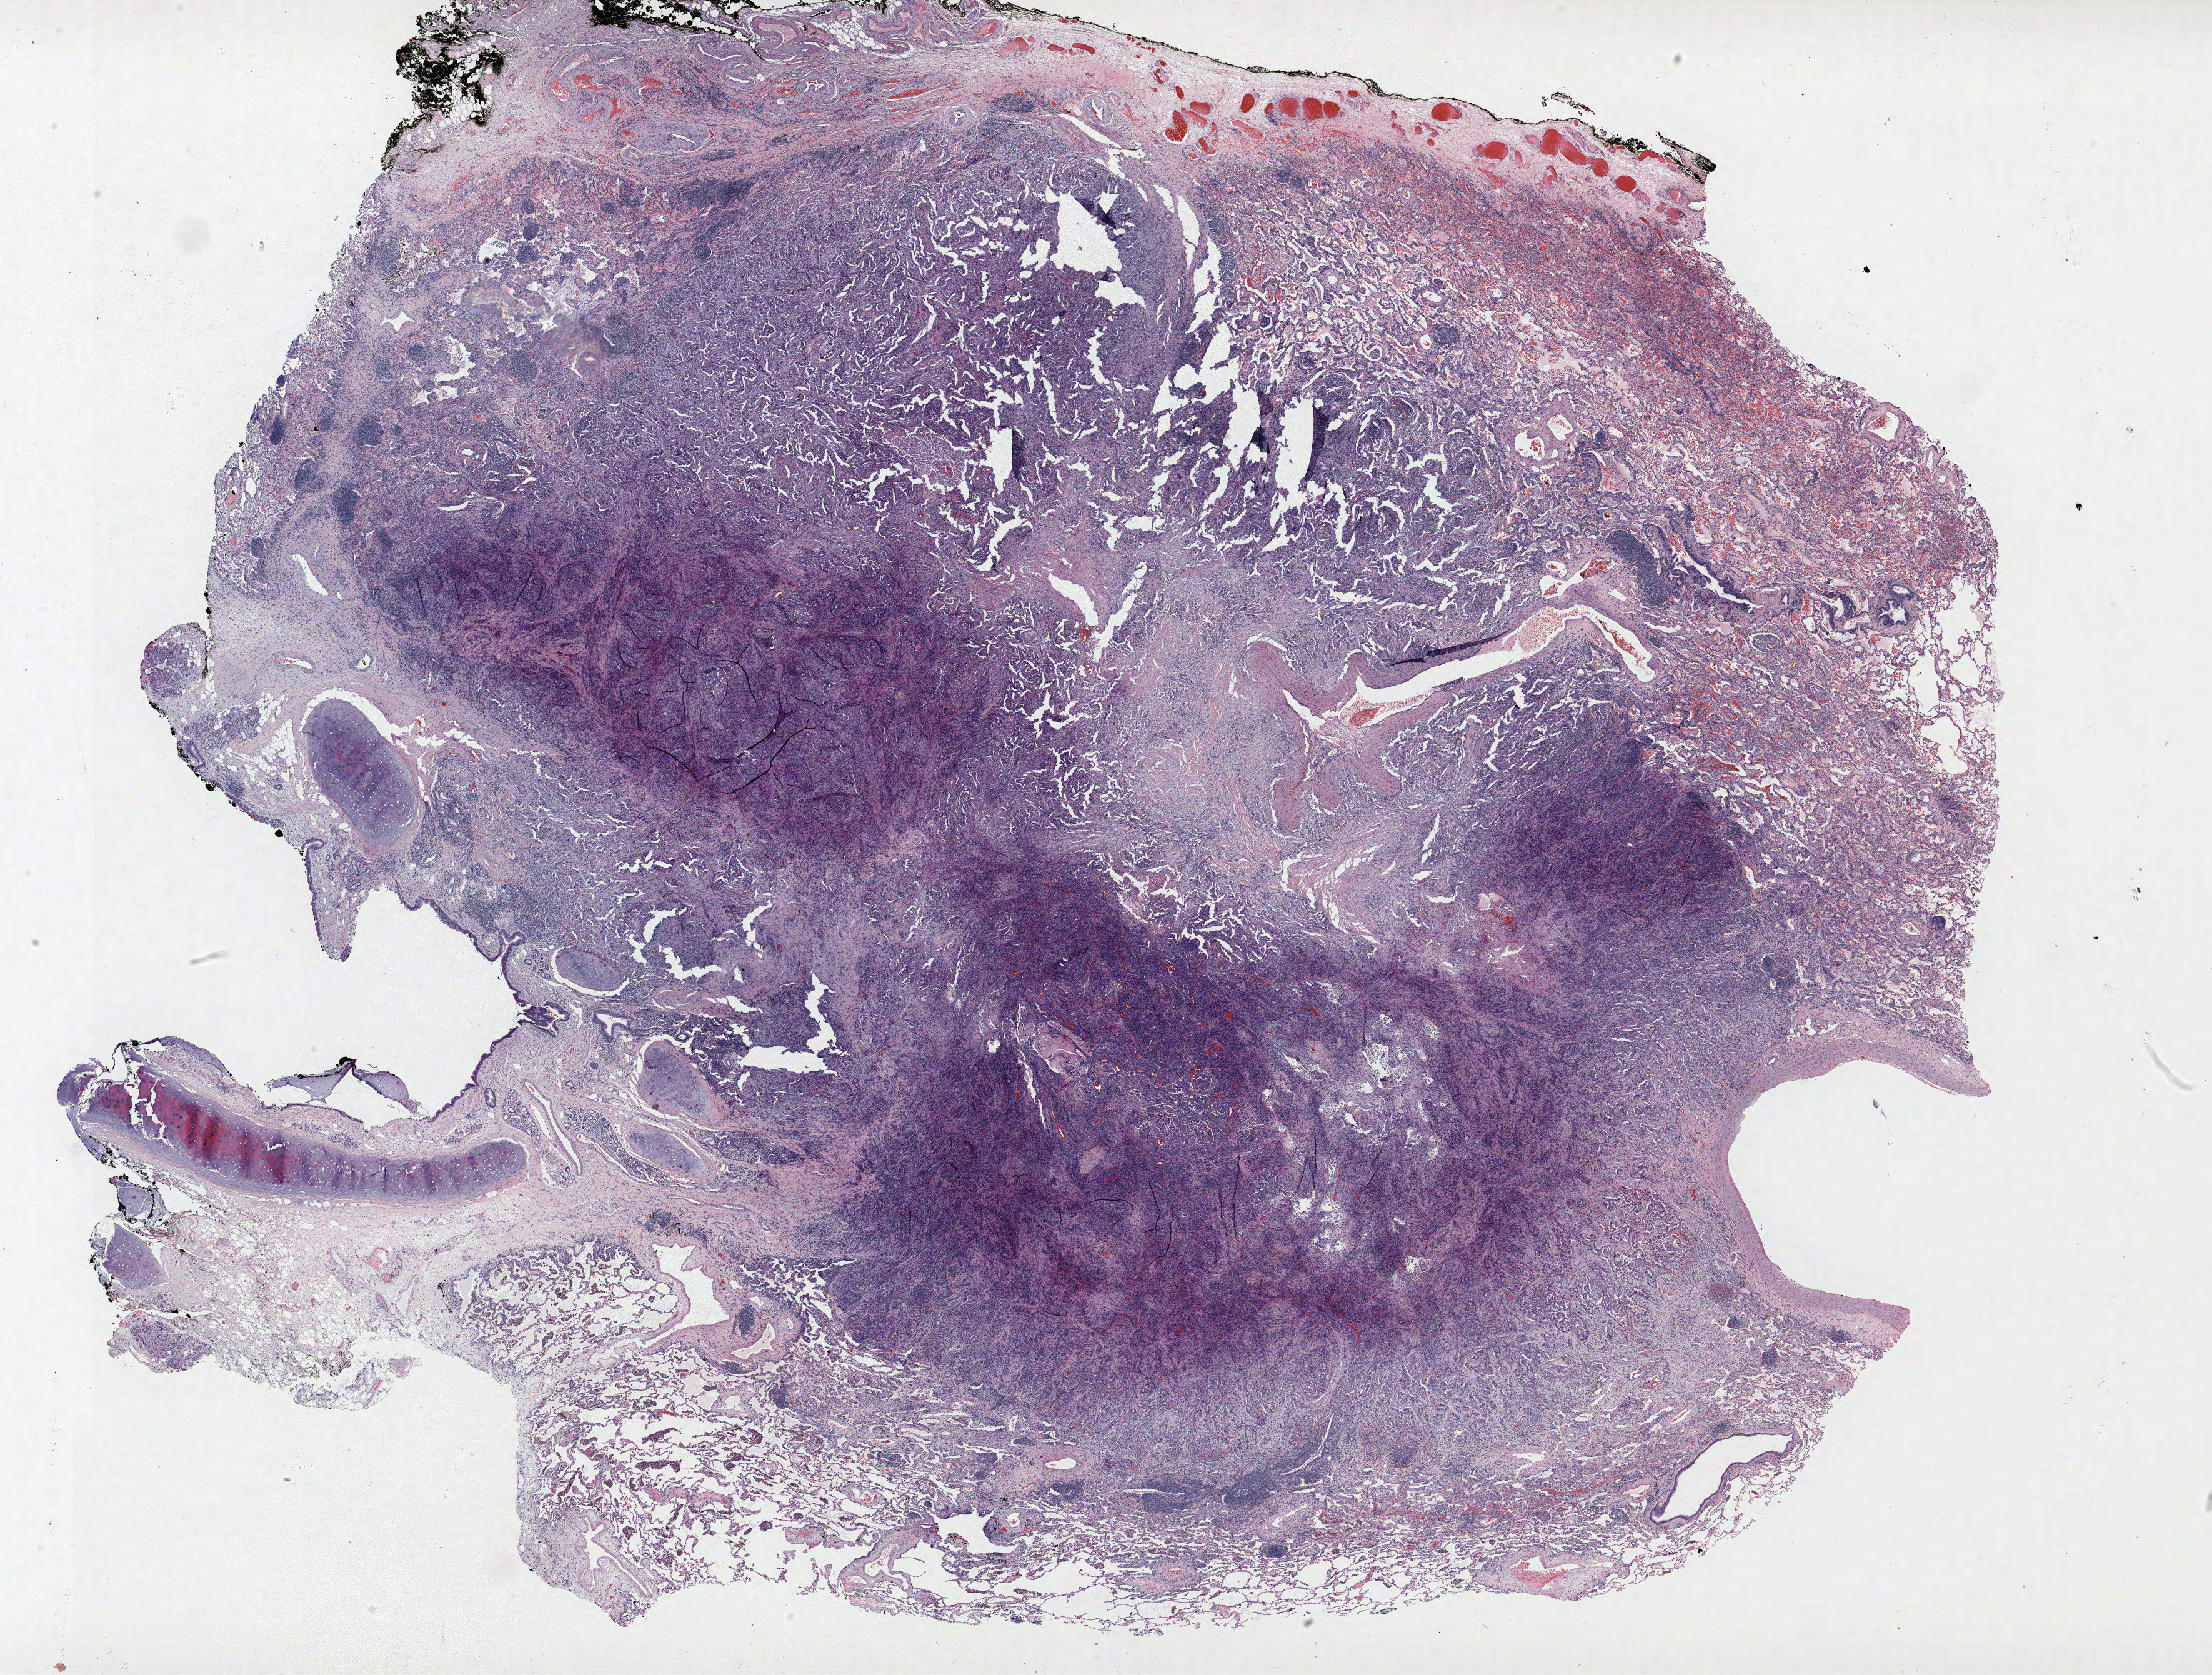
Whole-slide histology image, H&E-stained — low-resolution overview of the scanned area, about 28.3 x 21.4 mm, FFPE section, lung. Male, age 64 at enrolment. Former smoker at enrolment. Grade: poorly differentiated (G3).
* ICD-O-3 topography: upper lobe of lung (C34.1)
* stage (AJCC 6th edition): IA
* primary tumour location (clinical record): right upper lobe
* tumour size (pathology): 5 mm
* participant's lung-cancer diagnosis: Bronchiolo-alveolar adenocarcinoma, NOS
* note: participant had 2 primary lung cancers recorded; fields above describe the first